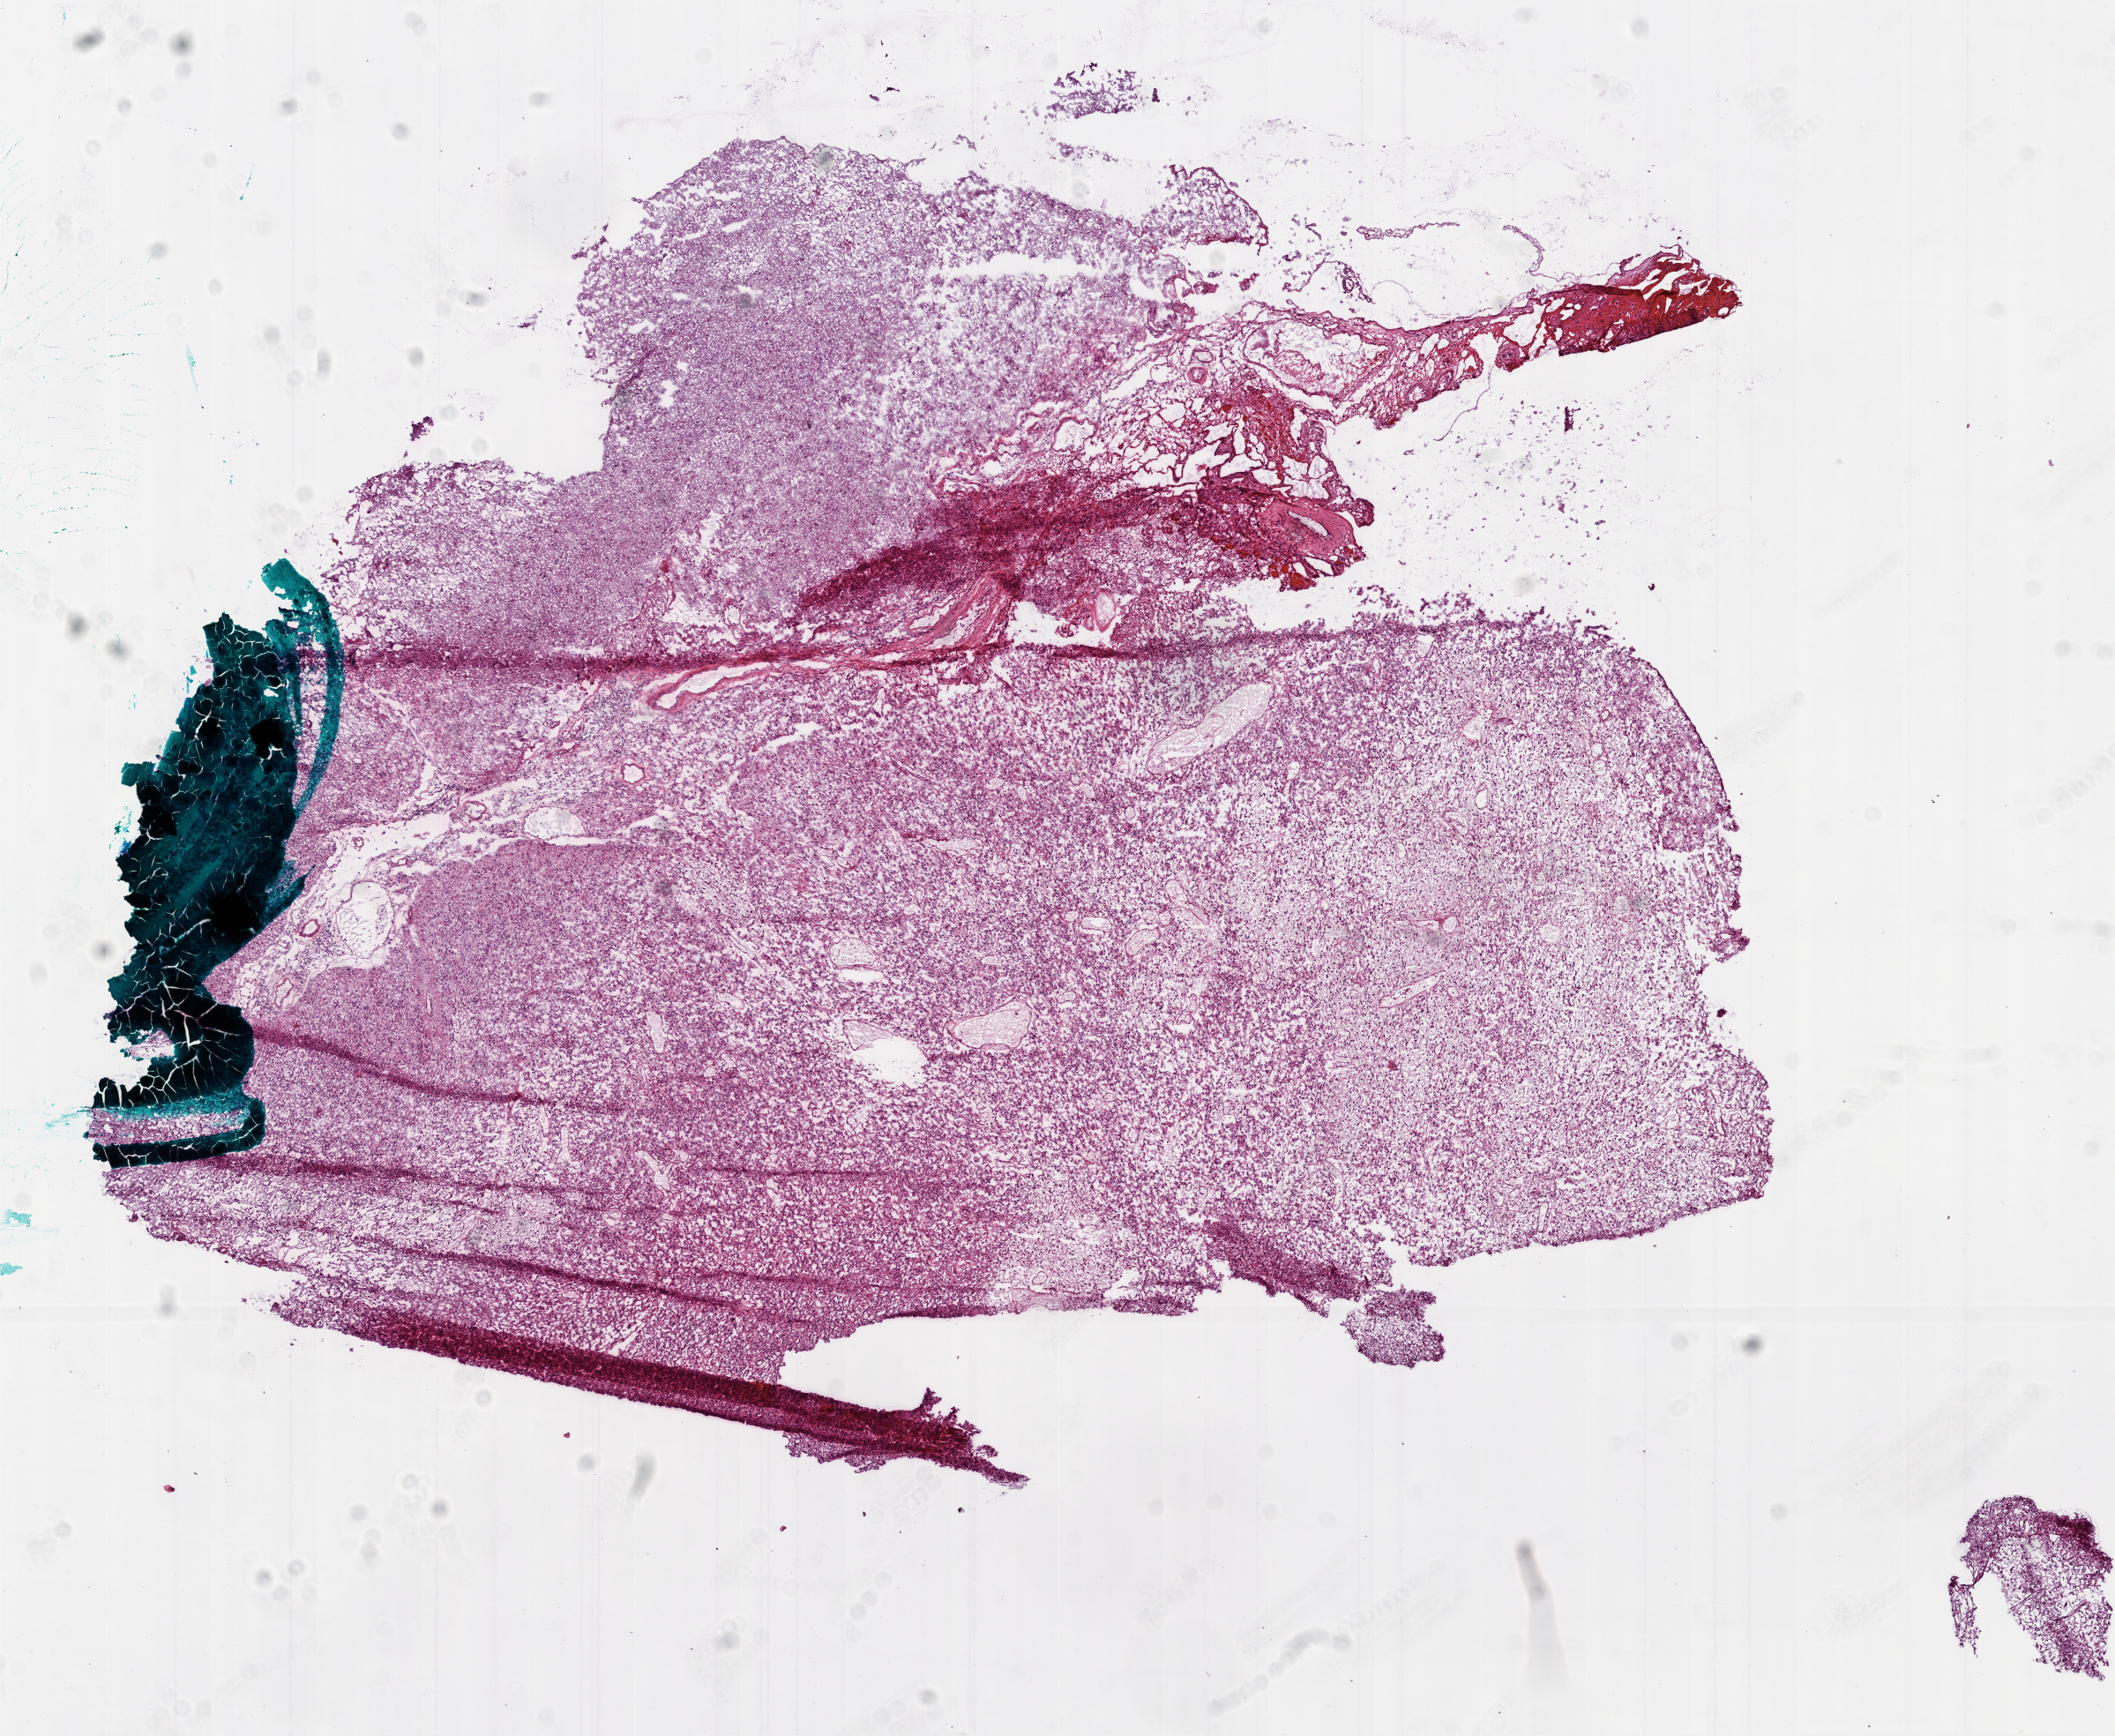
Digitized Hematoxylin and eosin (H&E) stained tissue section (whole slide), shown as a low-resolution overview of the whole scanned area (about 9.7 x 7.9 mm, from a 20x scan); frozen section; brain, primary tumour sample. Female patient; age at initial diagnosis 56 years. Pathologist review of this section (percent, as recorded): tumour cells 85%, tumour nuclei 90%, normal cells 0%, stromal cells 10%, necrosis 5%.
Diagnosis: Glioblastoma.